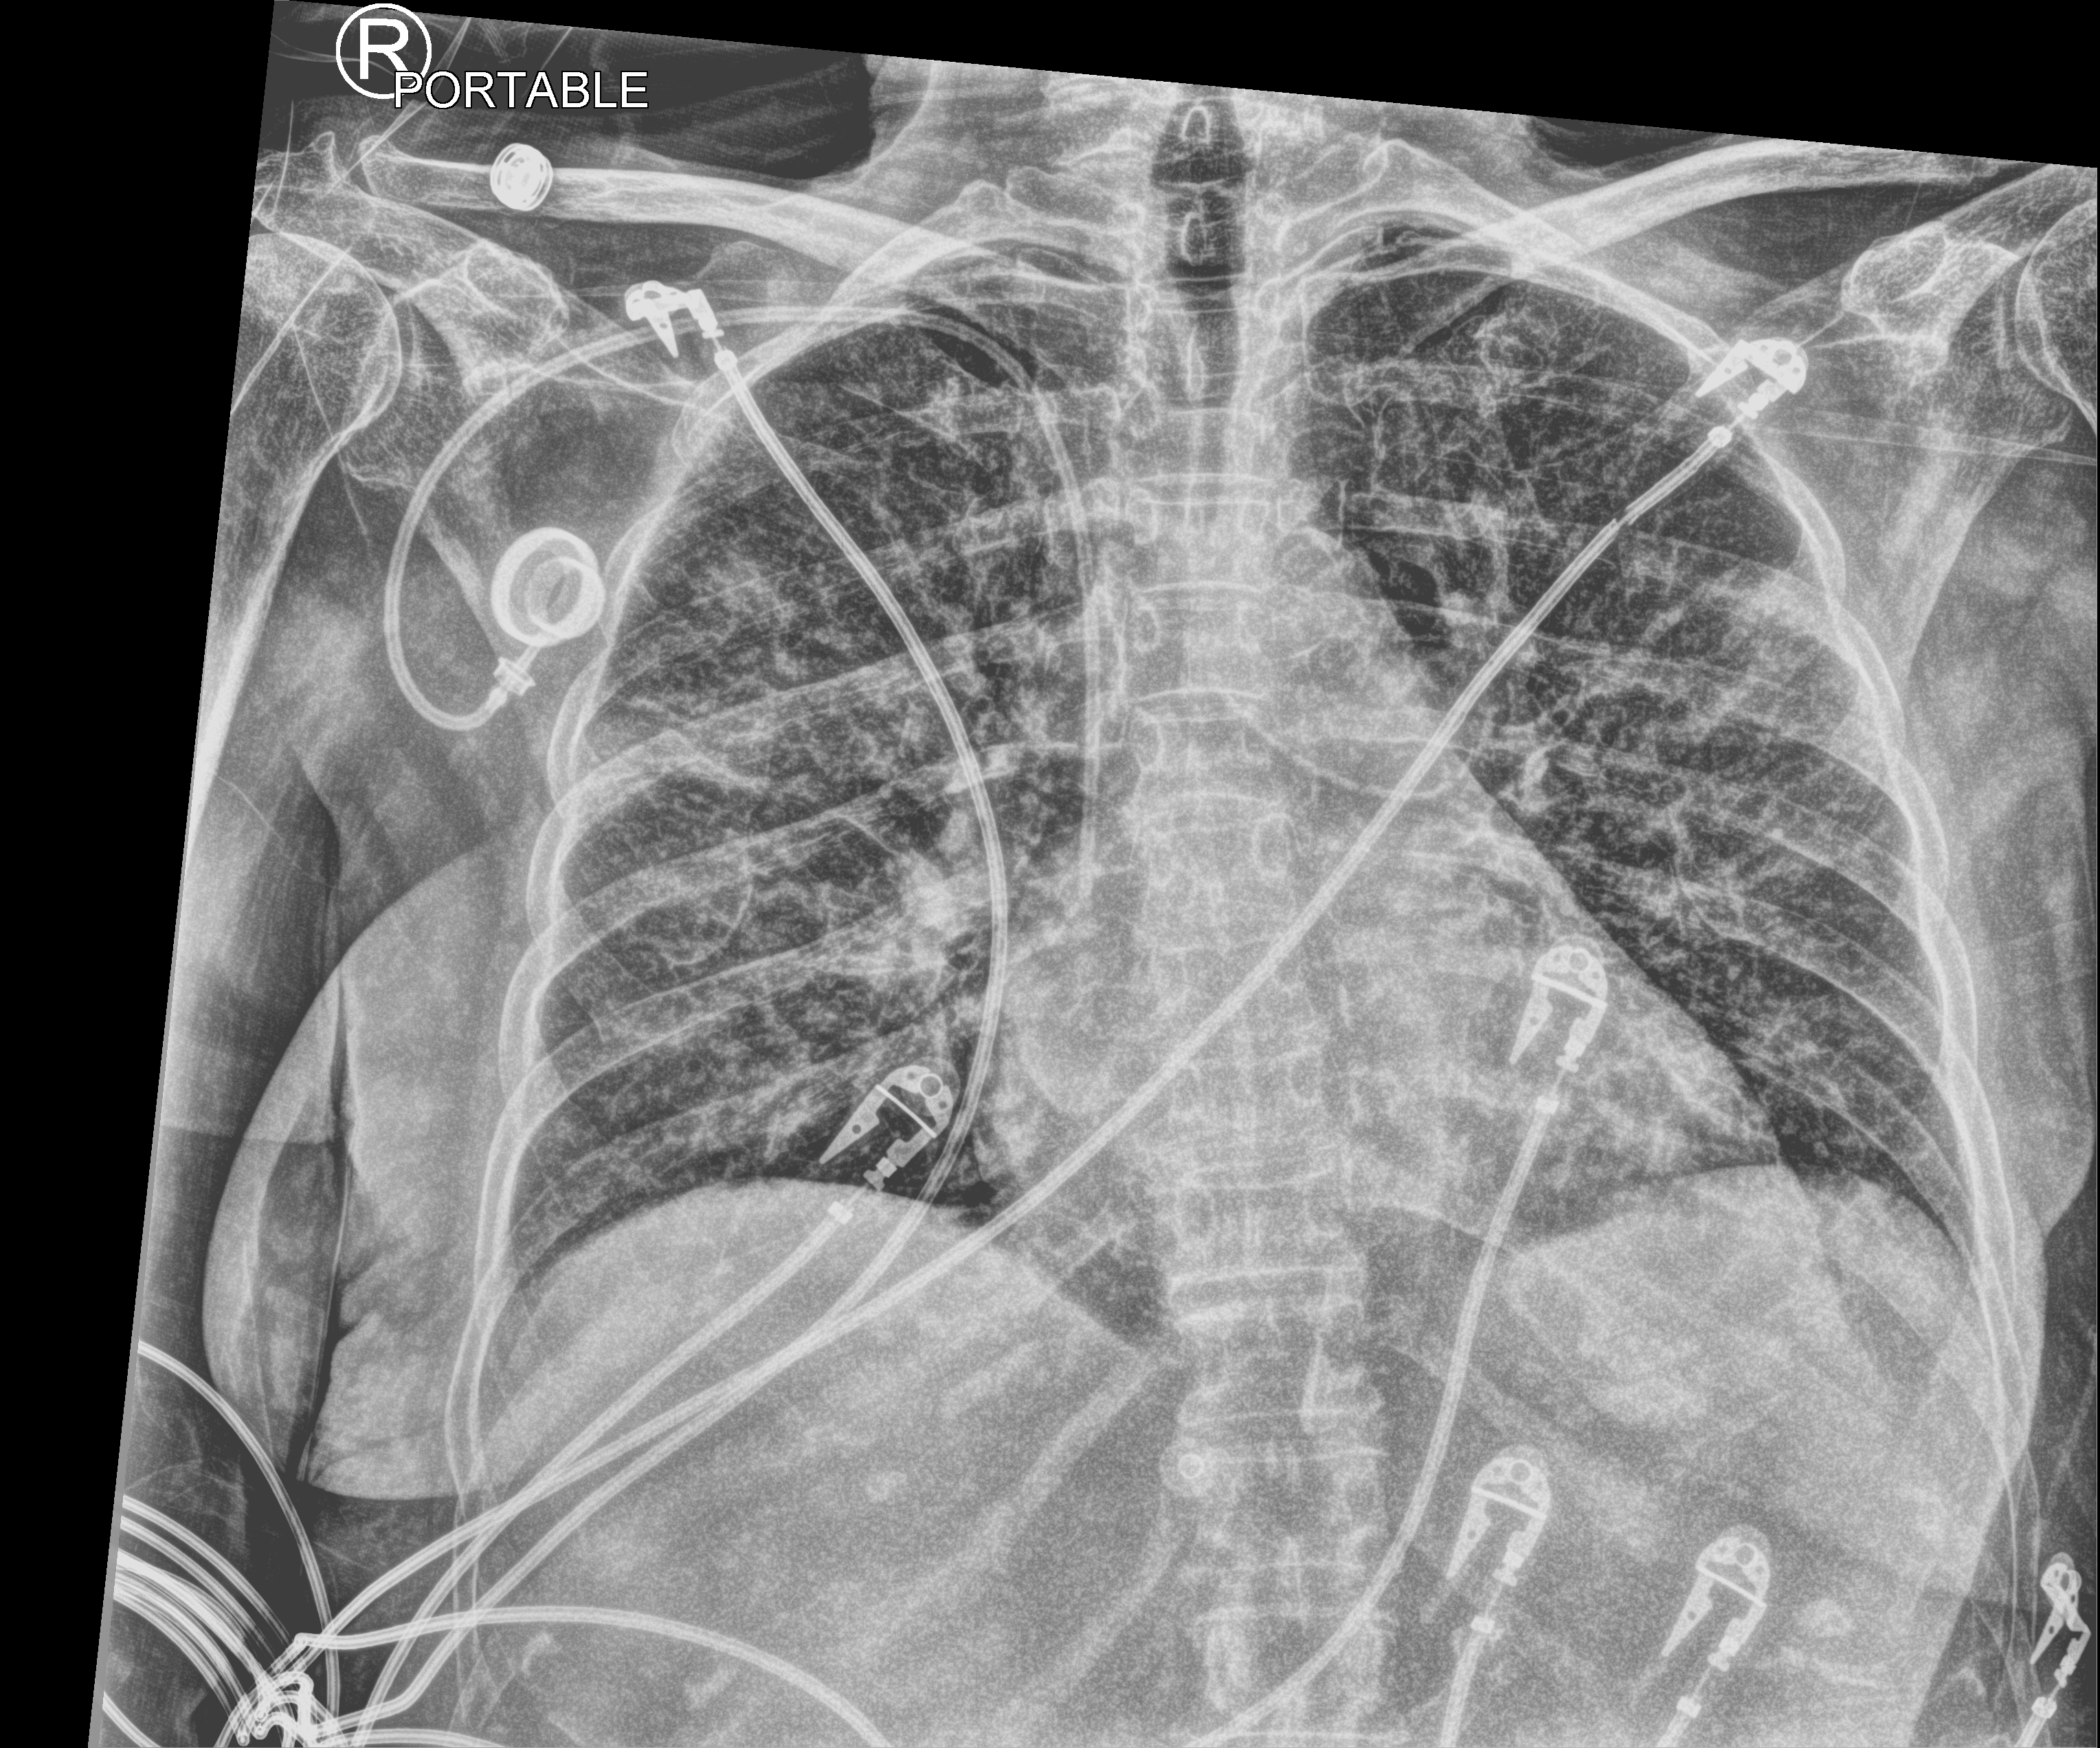
Chest X-ray (portable), anteroposterior (AP) projection. Patient hospitalised with COVID-19; female, aged 75–90 years.
Admission-level facts for this patient (not findings on this image; timing relative to this image not recorded):
- admitted to intensive care during this hospital stay: yes